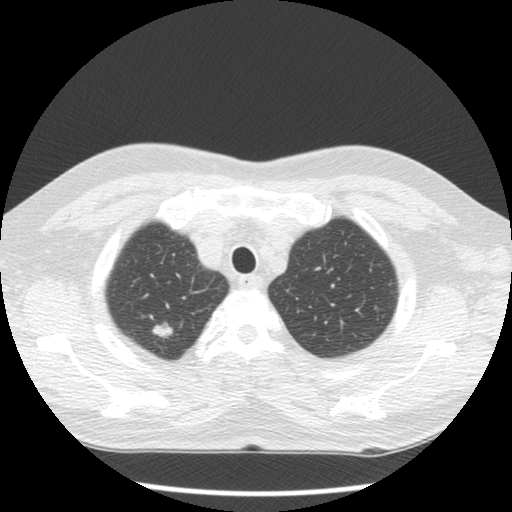
Low-dose screening chest CT, one axial slice; slice 103 of 120 in the series (ordered by position); 120 kVp; lung window (W 1500 / L -600 HU); 2.5 mm slice thickness; 512 × 512 image matrix, field of view 332 × 332 mm.
Outlined on this slice (expert manual segmentation):
- lesion 1 (tumor, upper lobe of right lung): bounding box [x1, y1, x2, y2] px = [153, 323, 173, 338]